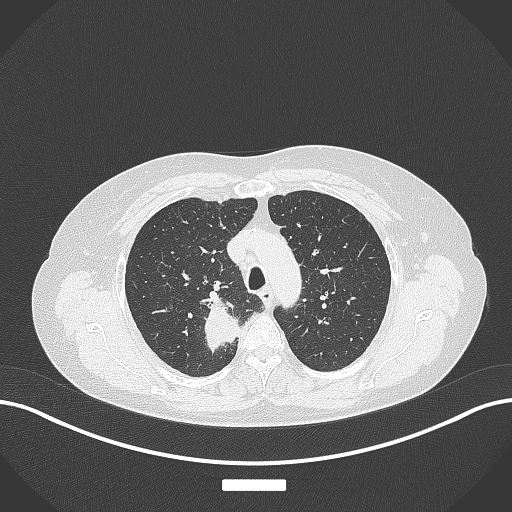
Chest CT, one axial slice; position 290 of 357 along the scan axis; 120 kVp; lung window (W 1500 / L -600 HU); 1 mm slice thickness; 512 × 512 image matrix, field of view 400 × 400 mm. Patient: female, 62 years. Case-level facts recorded for this patient, not image findings: clinical TNM (as recorded): T1c N1 M0.
Annotated regions visible in this slice (rectangle marked by the reading radiologist):
- lung tumour (recorded histology: squamous cell carcinoma): bounding box <197,296,241,357> (left, top, right, bottom; pixels)